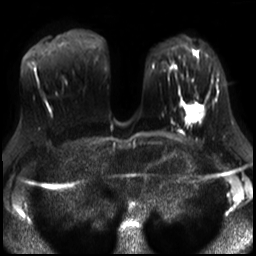
Breast MRI, one axial slice; position 13 of 30 along the scan axis; diffusion-weighted series; image 2 of 4 stored at this slice position (different b-values; order by instance number); 3 T; 4 mm slice thickness; 256 × 256 image matrix, field of view 320 × 320 mm. Female patient.
Structures marked on this image (expert manual segmentation):
- tumour on diffusion-weighted imaging: bounding box <186,104,200,119> (left, top, right, bottom; pixels)